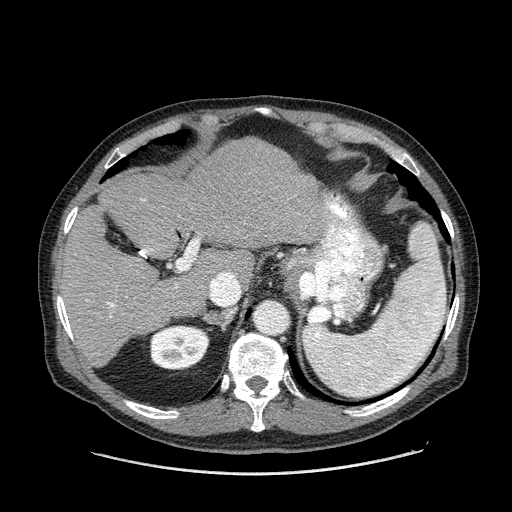
Contrast-enhanced abdominal CT (liver protocol), one axial slice. Slice 100 of 180 in the series (ordered by position). 120 kVp. One of 2 acquisitions stored at this slice position. Soft-tissue window (W 400 / L 40 HU). 2.5 mm slice thickness. 512 × 512 image matrix, field of view 420 × 420 mm. From the clinical record (not read from this slice): diagnosis: hepatocellular carcinoma (patient treated with transarterial chemoembolisation; whether this scan precedes or follows treatment is not stated here); TNM stage (as recorded): Stage-II; Child-Pugh class: A; tumour differentiation: well differentiated; tumour nodularity: multinodular.
Structures marked on this image (semi-automatic segmentation, software-assisted and operator-edited):
- liver parenchyma outside the tumour (the mass and vessels are separate outlines, so this box may not span the whole liver): bounding box [x1, y1, x2, y2] px = [58, 138, 328, 366]
- liver vessels: [69, 199, 178, 338]